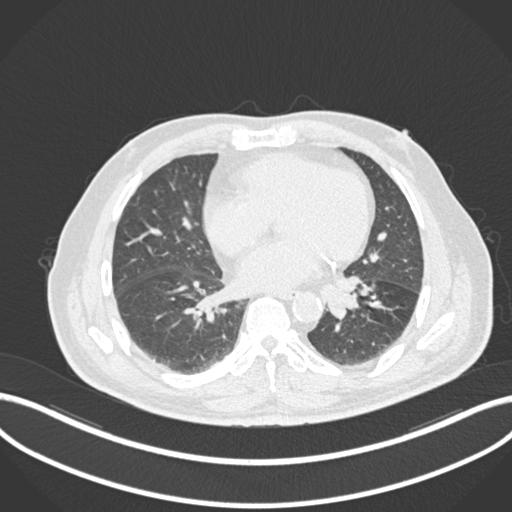
Chest CT, one axial slice. Position 48 of 161 along the scan axis. Reconstruction kernel B30f. Lung window (W 1500 / L -600 HU). 1 mm slice thickness. 512 × 512 image matrix, field of view 400 × 400 mm. Patient: male, 71 years. Case-level facts recorded for this patient, not image findings: clinical TNM (as recorded): T1b N0 M0.
Outlined on this slice (rectangle marked by the reading radiologist):
- lung tumour (recorded histology: squamous cell carcinoma): bounding box <330,275,368,323> (left, top, right, bottom; pixels)